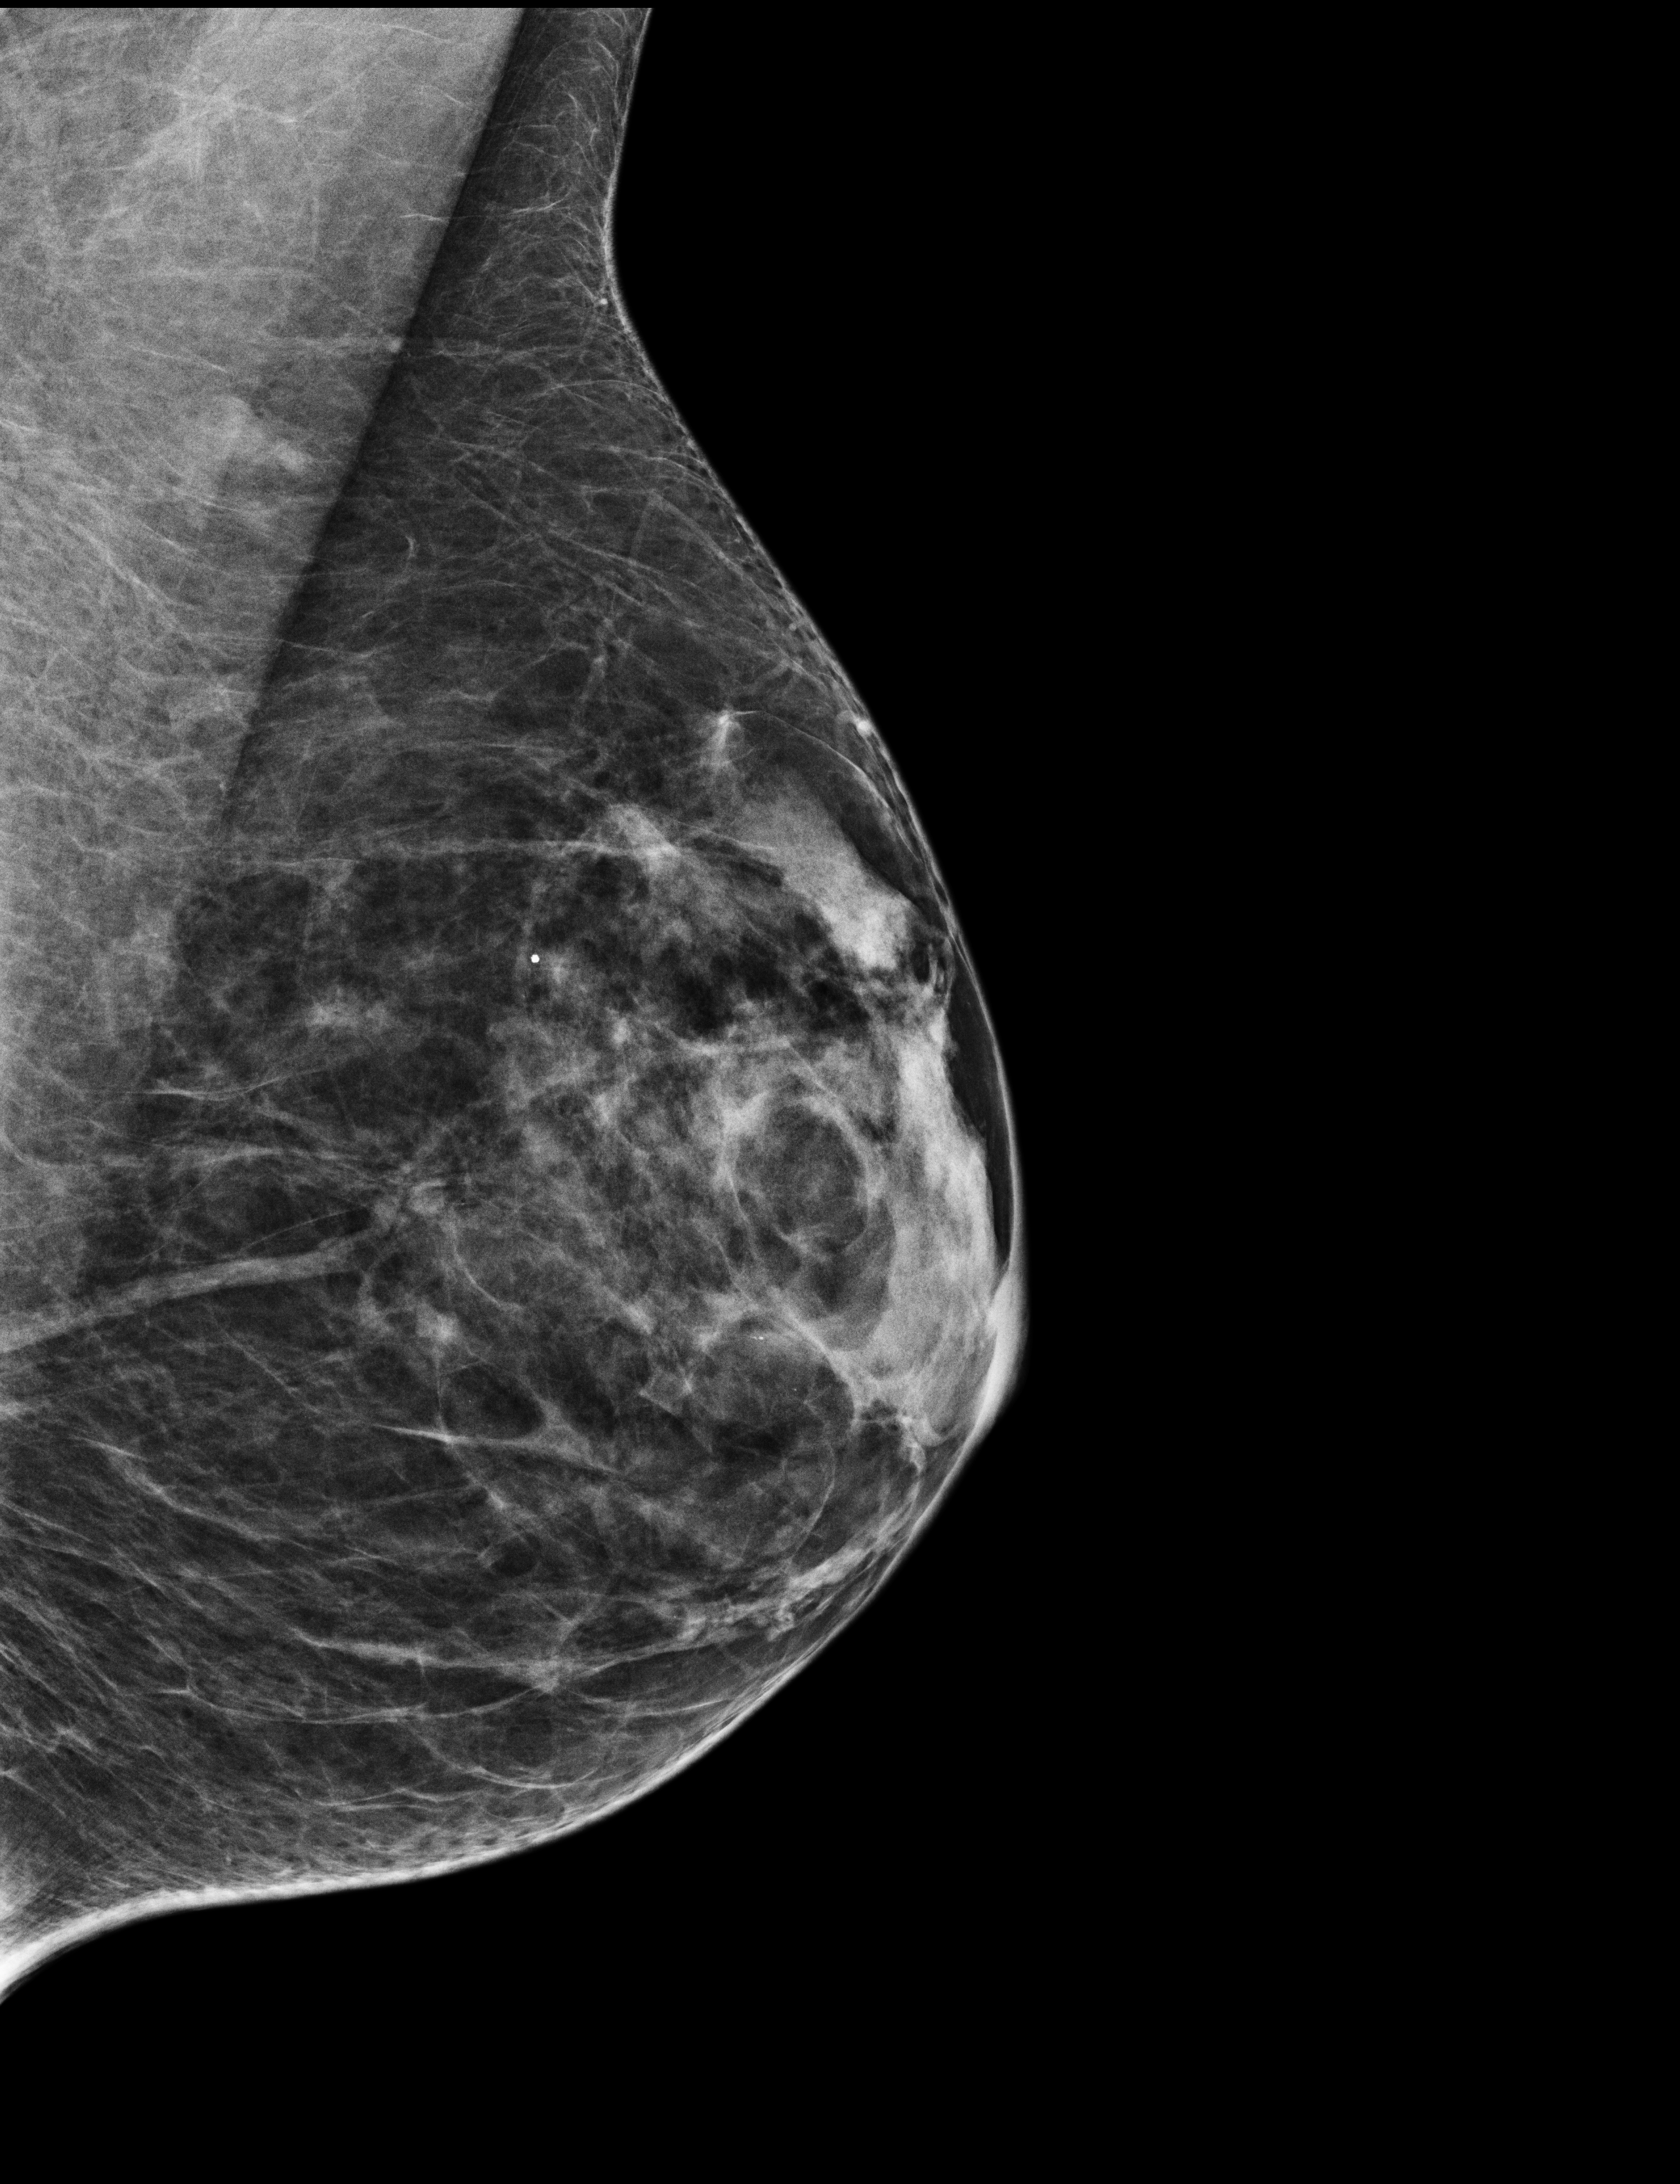
Diagnostic examination (additional views).
Image type: full-field digital mammogram. Breast: left. Projection: medio-lateral oblique projection.